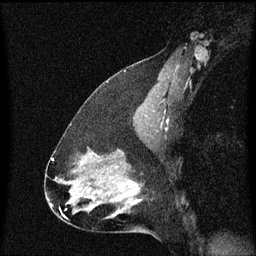
Breast MRI (dynamic contrast-enhanced), one sagittal slice. Position 39 of 60 along the scan axis. Dynamic contrast-enhanced series, image 2 of 3 at this slice position (ordered by acquisition). 1.5 T. TE 4.2 ms, TR 8.4 ms. 2 mm slice thickness. 256 × 256 image matrix, field of view 200 × 200 mm. Female patient, age 47 years.
Annotated regions visible in this slice (semi-automatically segmented with operator editing):
- analysis volume of interest (the breast-tissue region the enhancement analysis was run in; not a lesion): bounding box (x1, y1, x2, y2) in pixels: (100, 172, 146, 219)
- tumour enhancement mask (voxels above the 70 % enhancement threshold inside the analysis volume of interest): (120, 182, 141, 205)